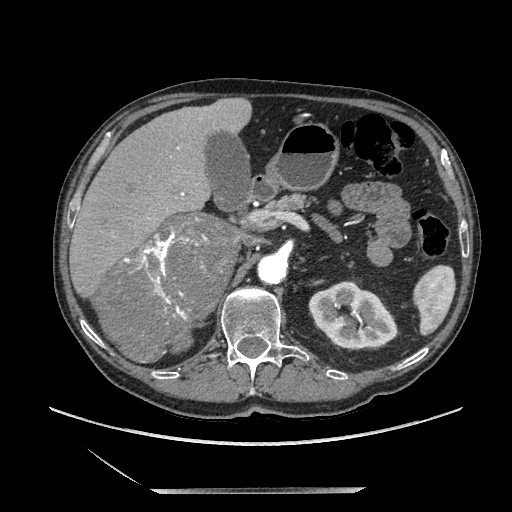
Contrast-enhanced abdominal CT, one axial slice. Slice 123 of 243 in the series (ordered by position). Soft-tissue window (W 400 / L 40 HU). 1.25 mm slice thickness. 512 × 512 image matrix, field of view 420 × 420 mm. Male patient. From the clinical record (not read from this slice): diagnosis: adrenocortical carcinoma; tumour side: right adrenal; tumour size at pathology: 16 cm; Ki-67 index: 17 %; stage (as recorded): 3.
Structures marked on this image (semi-automatically segmented with operator editing):
- mass: box from (x=99, y=214) to (x=239, y=362) px